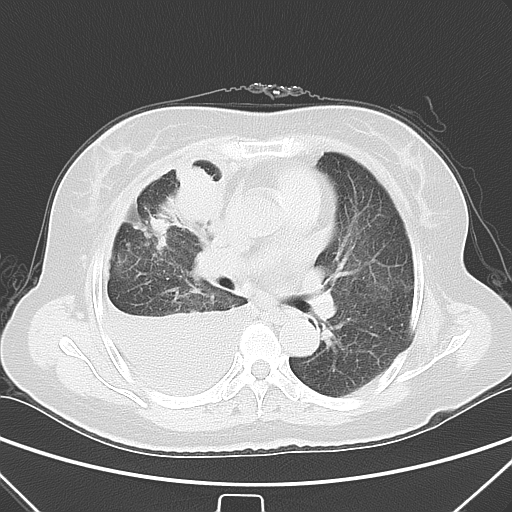
Chest CT, one axial slice. Slice 34 of 55 in the series (ordered by position). 120 kVp. Lung window (W 1500 / L -600 HU). 5 mm slice thickness. 512 × 512 image matrix, field of view 352 × 352 mm. Female patient, age 66 years. Case-level facts recorded for this patient, not image findings: clinical TNM (as recorded): T2 N0 M1.
Structures marked on this image (bounding box drawn by a radiologist):
- lung tumour (recorded histology: adenocarcinoma): bounding box [x1, y1, x2, y2] px = [159, 163, 225, 224]